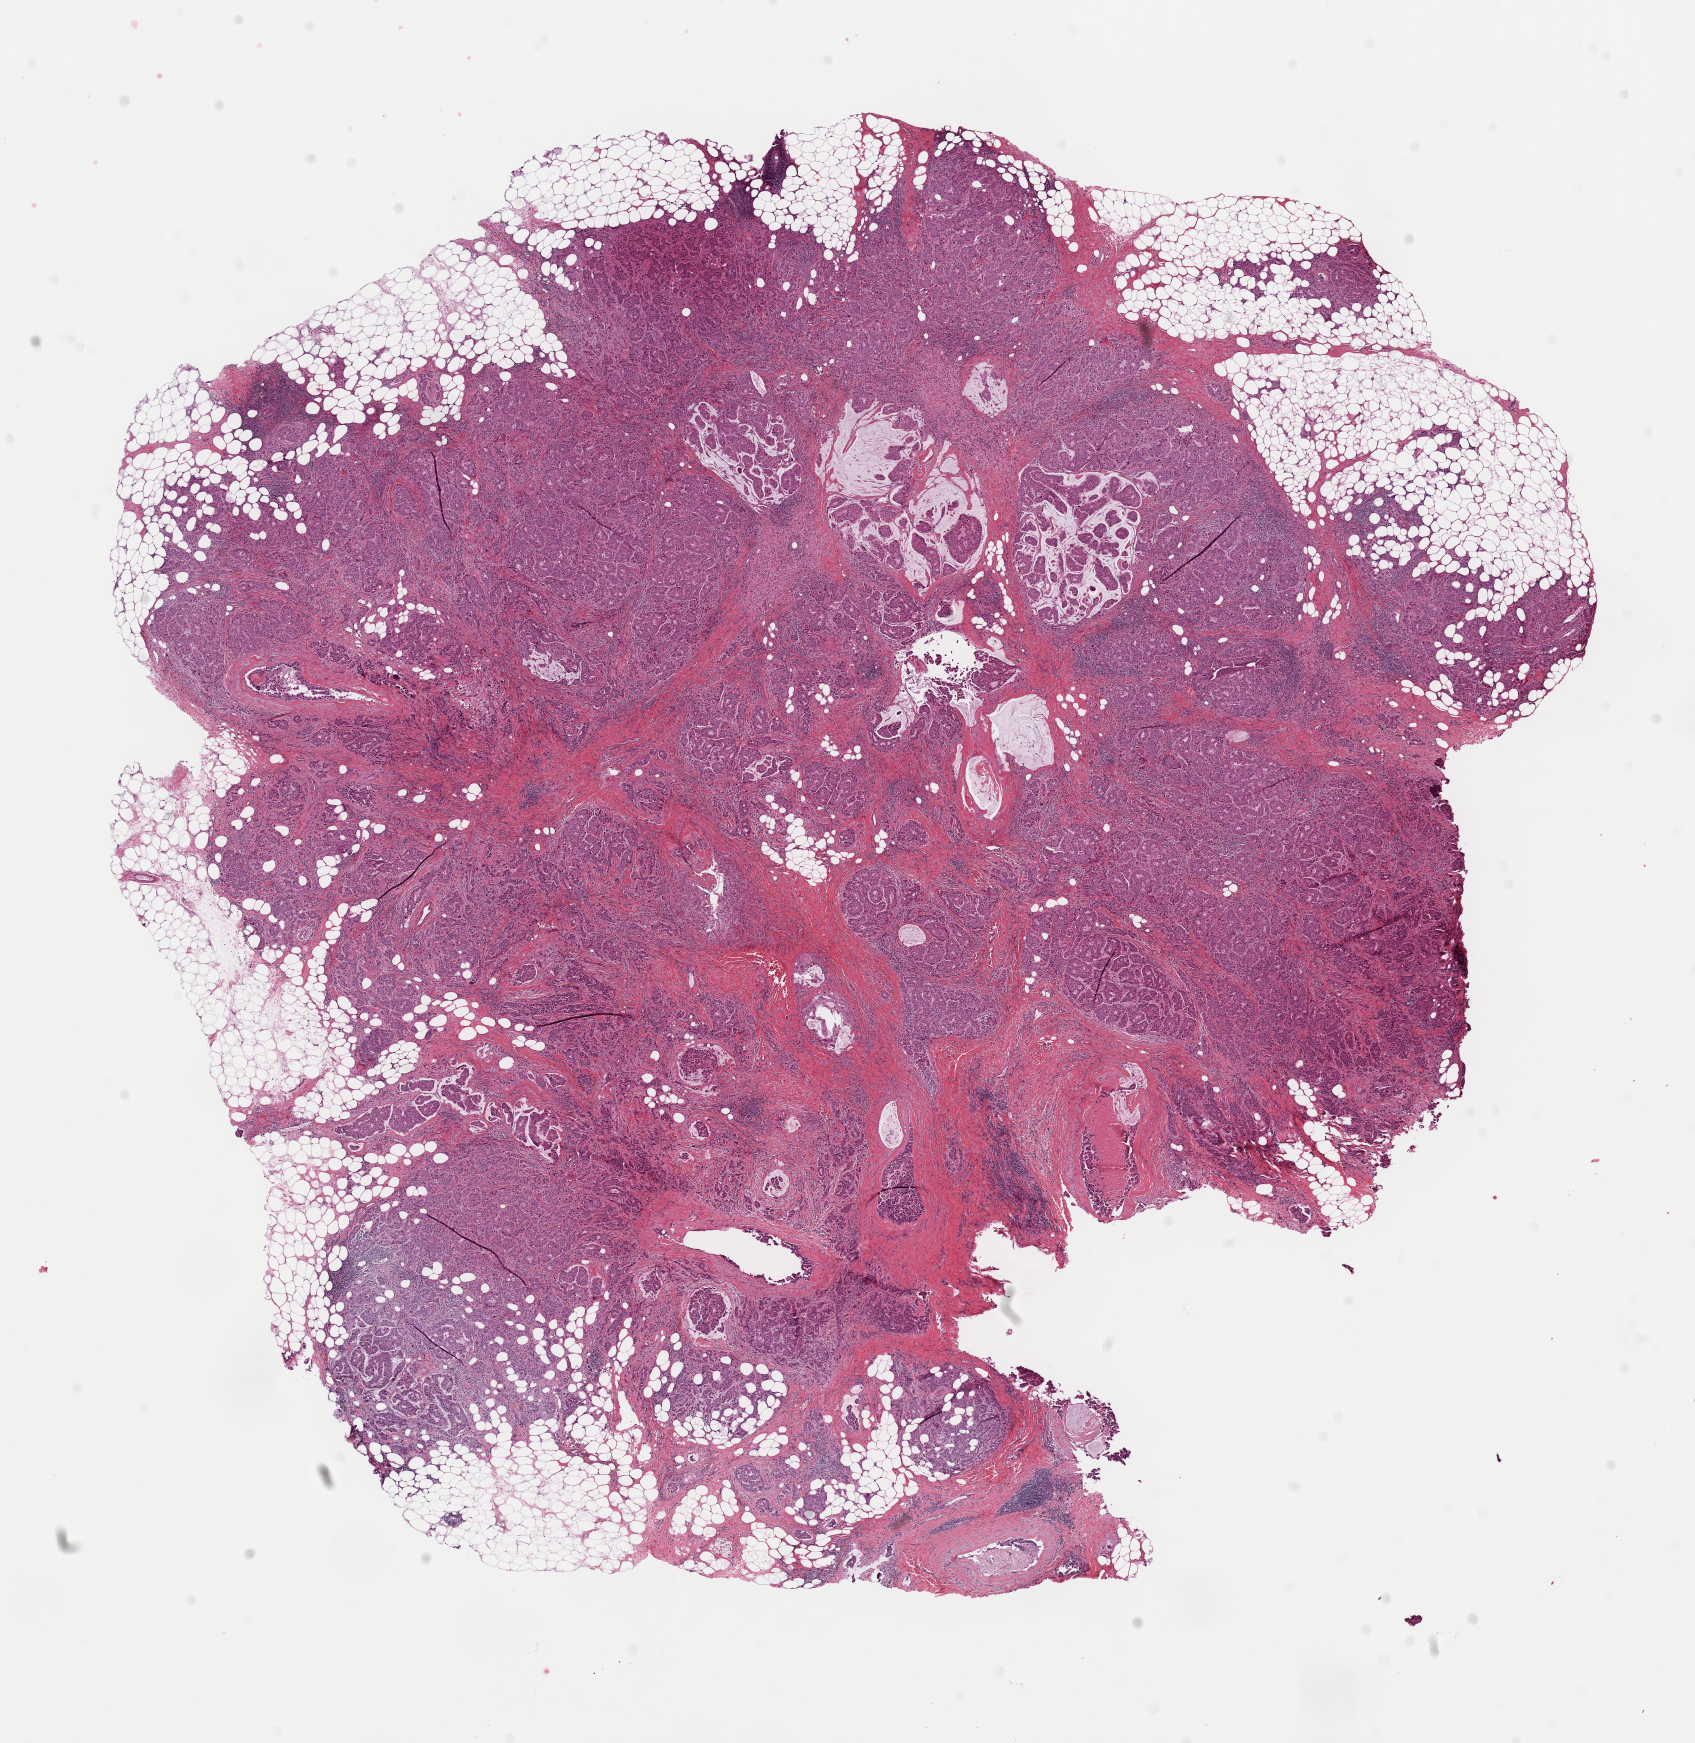
Digitized H&E-stained tissue section (whole slide) — a low-resolution overview of the entire scanned area, about 13.4 x 13.8 mm (from a 40x scan), formalin-fixed paraffin-embedded (FFPE) diagnostic section, primary tumour sample from the breast. Female patient; age at initial diagnosis 27 years.
Histologic diagnosis: Infiltrating duct carcinoma, NOS.